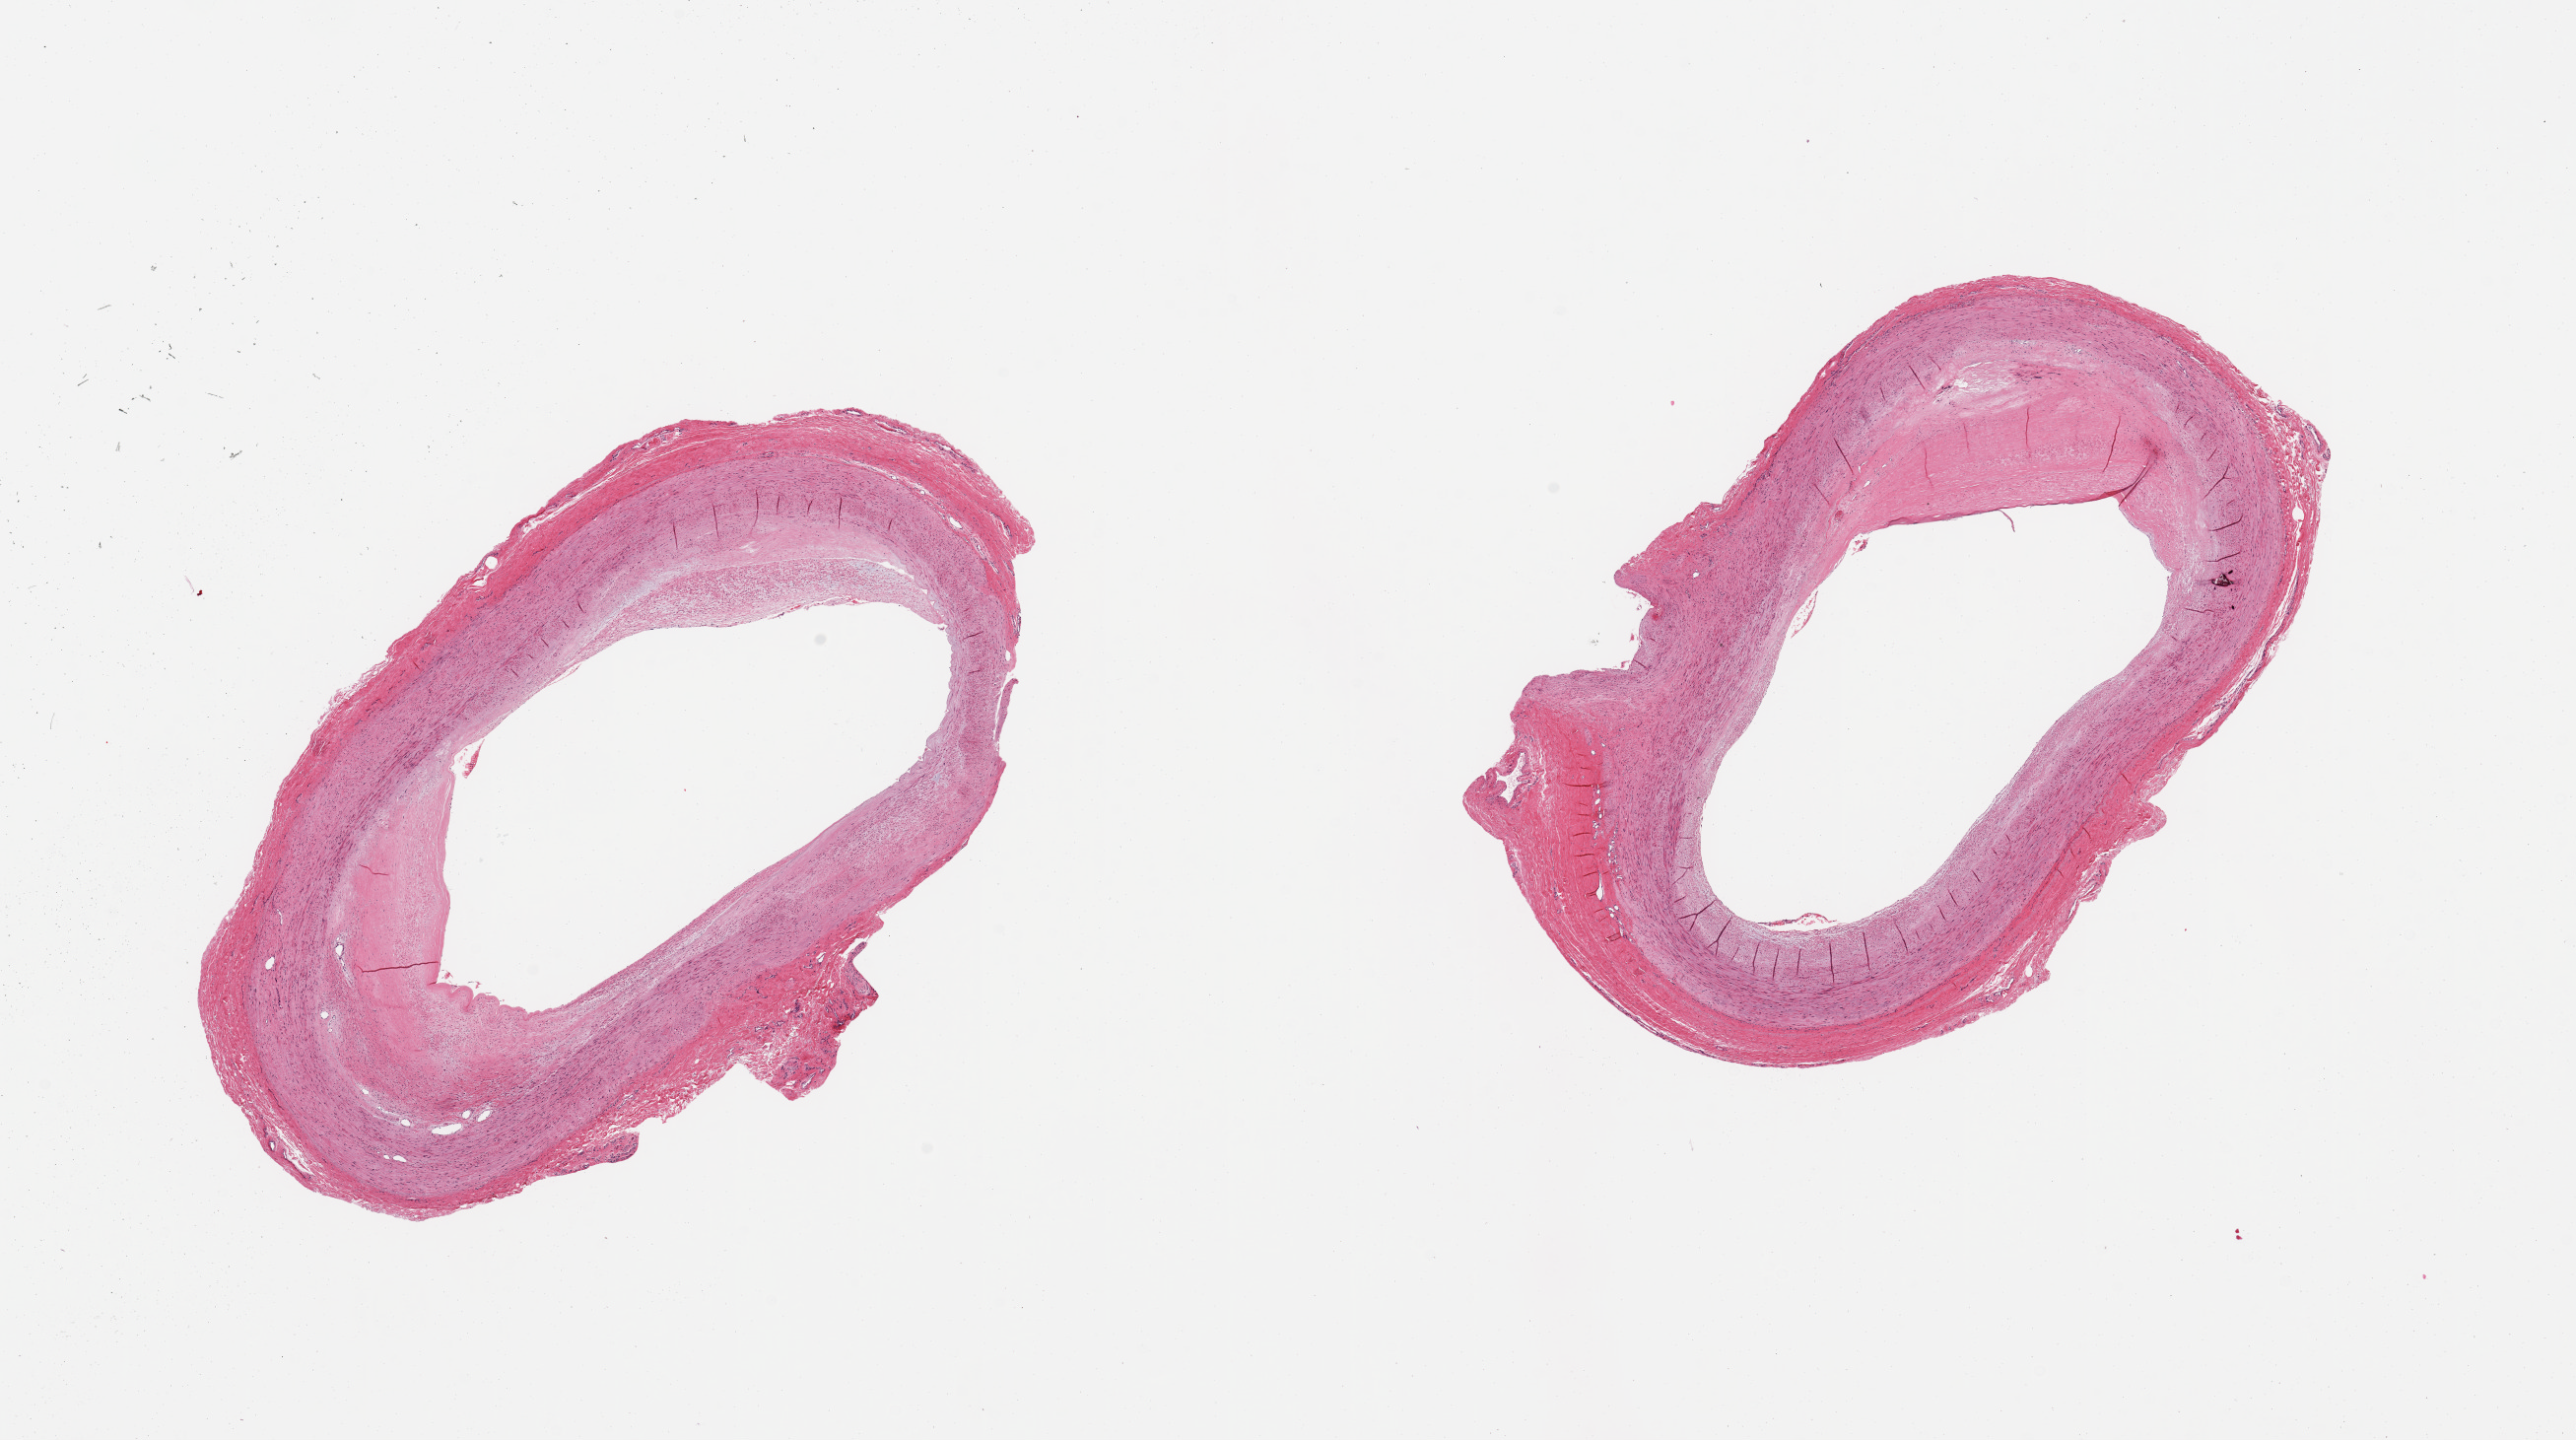
Digitized H&E-stained section, brightfield, low-resolution overview of the scanned area, about 20.7 x 11.6 mm (acquisition: 20x scan). PAXgene-fixed, paraffin-embedded tissue. Sampled site (target tissue): tibial artery. Donor tissue sample. Donor sex: male.
Reviewer comment on this tissue sample: 2 pieces, ath atherosis occludes ~30% of lumen.